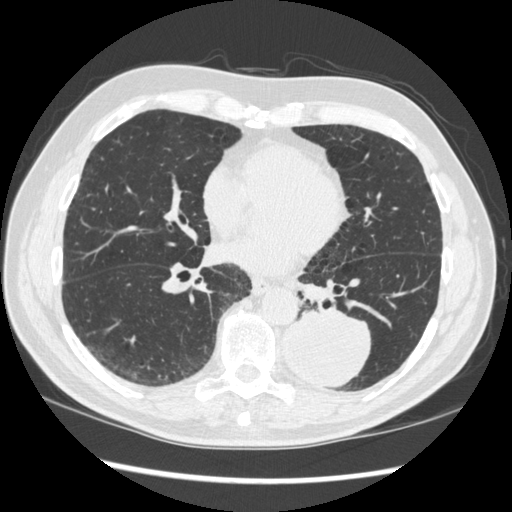
Low-dose screening chest CT, one axial slice; slice 140 of 348 in the series (ordered by position); reconstruction kernel STANDARD; 120 kVp; lung window (W 1500 / L -600 HU); 1.25 mm slice thickness; 512 × 512 image matrix, field of view 360 × 360 mm.
Annotated regions visible in this slice (manually delineated by an expert):
- lesion 1 (tumor, lower lobe of left lung): box from (x=283, y=310) to (x=372, y=387) px